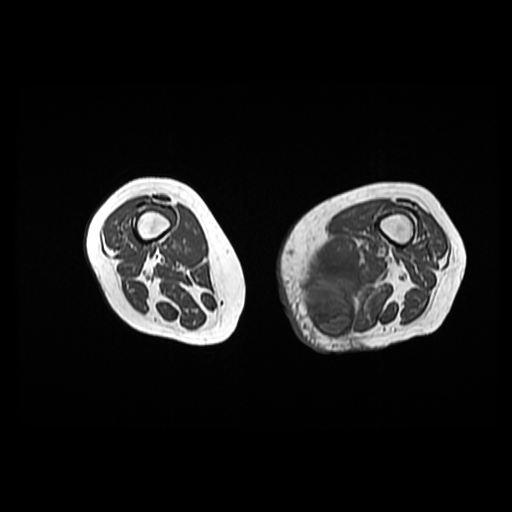
MRI of an extremity soft-tissue mass, one axial slice; position 24 of 42 along the scan axis; 512 × 512 image matrix, field of view 420 × 420 mm. Female patient. Case-level facts recorded for this patient, not image findings: histological type: pleomorphic leiomyosarcoma; grade: high; site of the primary tumour: left thigh.
Annotated regions visible in this slice (manually delineated by an expert):
- gross tumour volume including surrounding oedema: bounding box [x1, y1, x2, y2] px = [303, 241, 383, 340]
- gross tumour volume (mass): [303, 280, 354, 335]